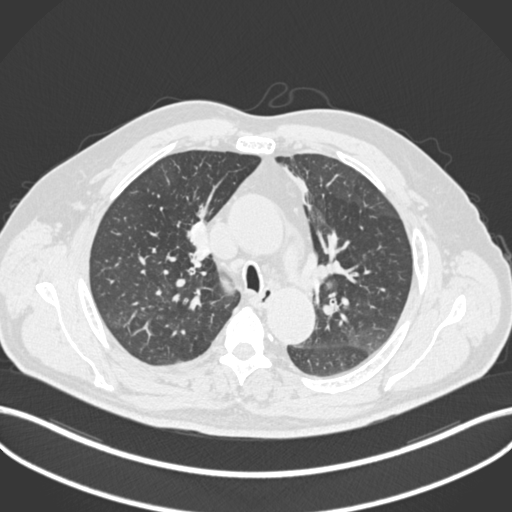
Chest CT, one axial slice; reconstruction kernel B30f; 120 kVp; lung window (W 1500 / L -600 HU); 512 × 512 image matrix. Male patient, age 60 years. From the clinical record (not read from this slice): clinical TNM (as recorded): T1b N1 M0.
Outlined on this slice (bounding box drawn by a radiologist):
- lung tumour (recorded histology: squamous cell carcinoma): bounding box (x1, y1, x2, y2) in pixels: (174, 208, 215, 268)